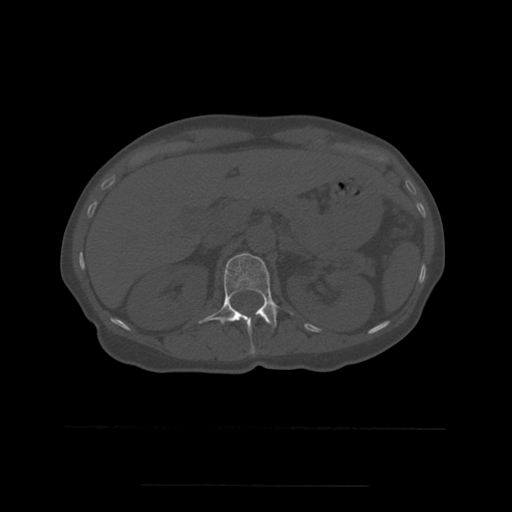
CT including the spine, one axial slice. Position 239 of 544 along the scan axis. Bone window (W 1800 / L 400 HU). 512 × 512 image matrix. Patient age 58 years. From the clinical record (not read from this slice): primary cancer: lung.
Outlined on this slice (semi-automatically segmented with operator editing):
- L1 vertebra: bounding box <199,253,278,354> (left, top, right, bottom; pixels)